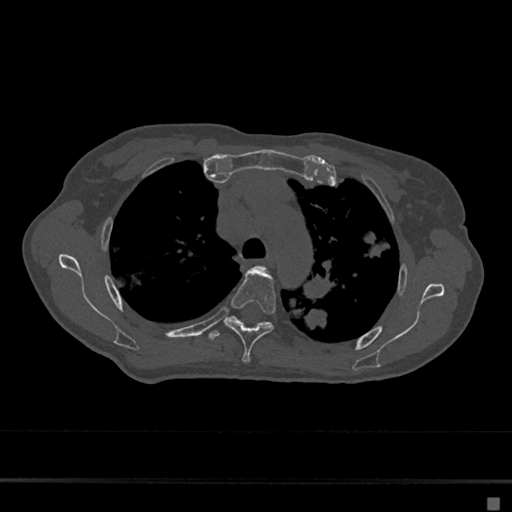
CT including the spine, one axial slice. Slice 494 of 797 in the series (ordered by position). Reconstruction kernel Br40s/3. Bone window (W 1800 / L 400 HU). 512 × 512 image matrix, field of view 360 × 360 mm. Patient: female, 68 years. Case-level facts recorded for this patient, not image findings: primary cancer: renal.
Annotated regions visible in this slice (semi-automatically segmented with operator editing):
- T4 vertebra: box from (x=224, y=269) to (x=276, y=363) px
- T5 vertebra: (x=208, y=315)–(x=271, y=340)